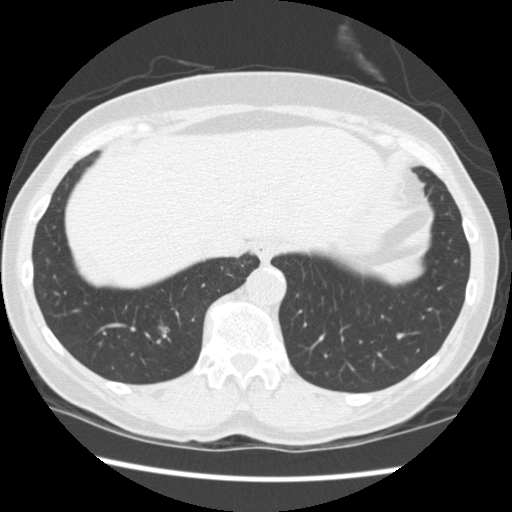
Low-dose screening chest CT, one axial slice. Slice 57 of 262 in the series (ordered by position). Reconstruction kernel STANDARD. Lung window (W 1500 / L -600 HU). 2.5 mm slice thickness. 512 × 512 image matrix.
Annotated regions visible in this slice (expert manual segmentation):
- lesion 1 (tumor, lower lobe of right lung): bounding box [x1, y1, x2, y2] px = [158, 330, 166, 343]